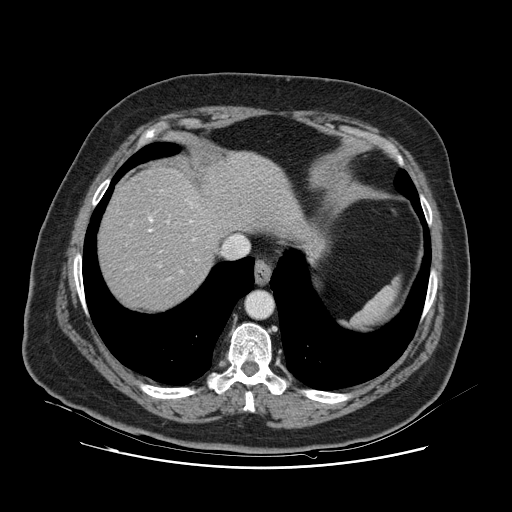
Contrast-enhanced abdominal CT, one axial slice; slice 104 of 132 in the series (ordered by position); 120 kVp; intravenous contrast given; soft-tissue window (W 400 / L 40 HU); 2.5 mm slice thickness; 512 × 512 image matrix, field of view 391 × 391 mm. Female patient, age 73 years. From the clinical record (not read from this slice): diagnosis: colorectal cancer liver metastases, imaged before liver resection; multiple liver metastases: no; largest metastasis: 7 cm; disease in both lobes: no.
Structures marked on this image (outlined manually by an expert reader):
- hepatic veins: box from (x=149, y=217) to (x=196, y=273) px
- liver: (x=100, y=154)–(x=295, y=309)
- planned liver remnant (the part of the liver to remain after resection): (x=100, y=168)–(x=225, y=309)
- portal vein (with intrahepatic branches): (x=160, y=221)–(x=169, y=267)